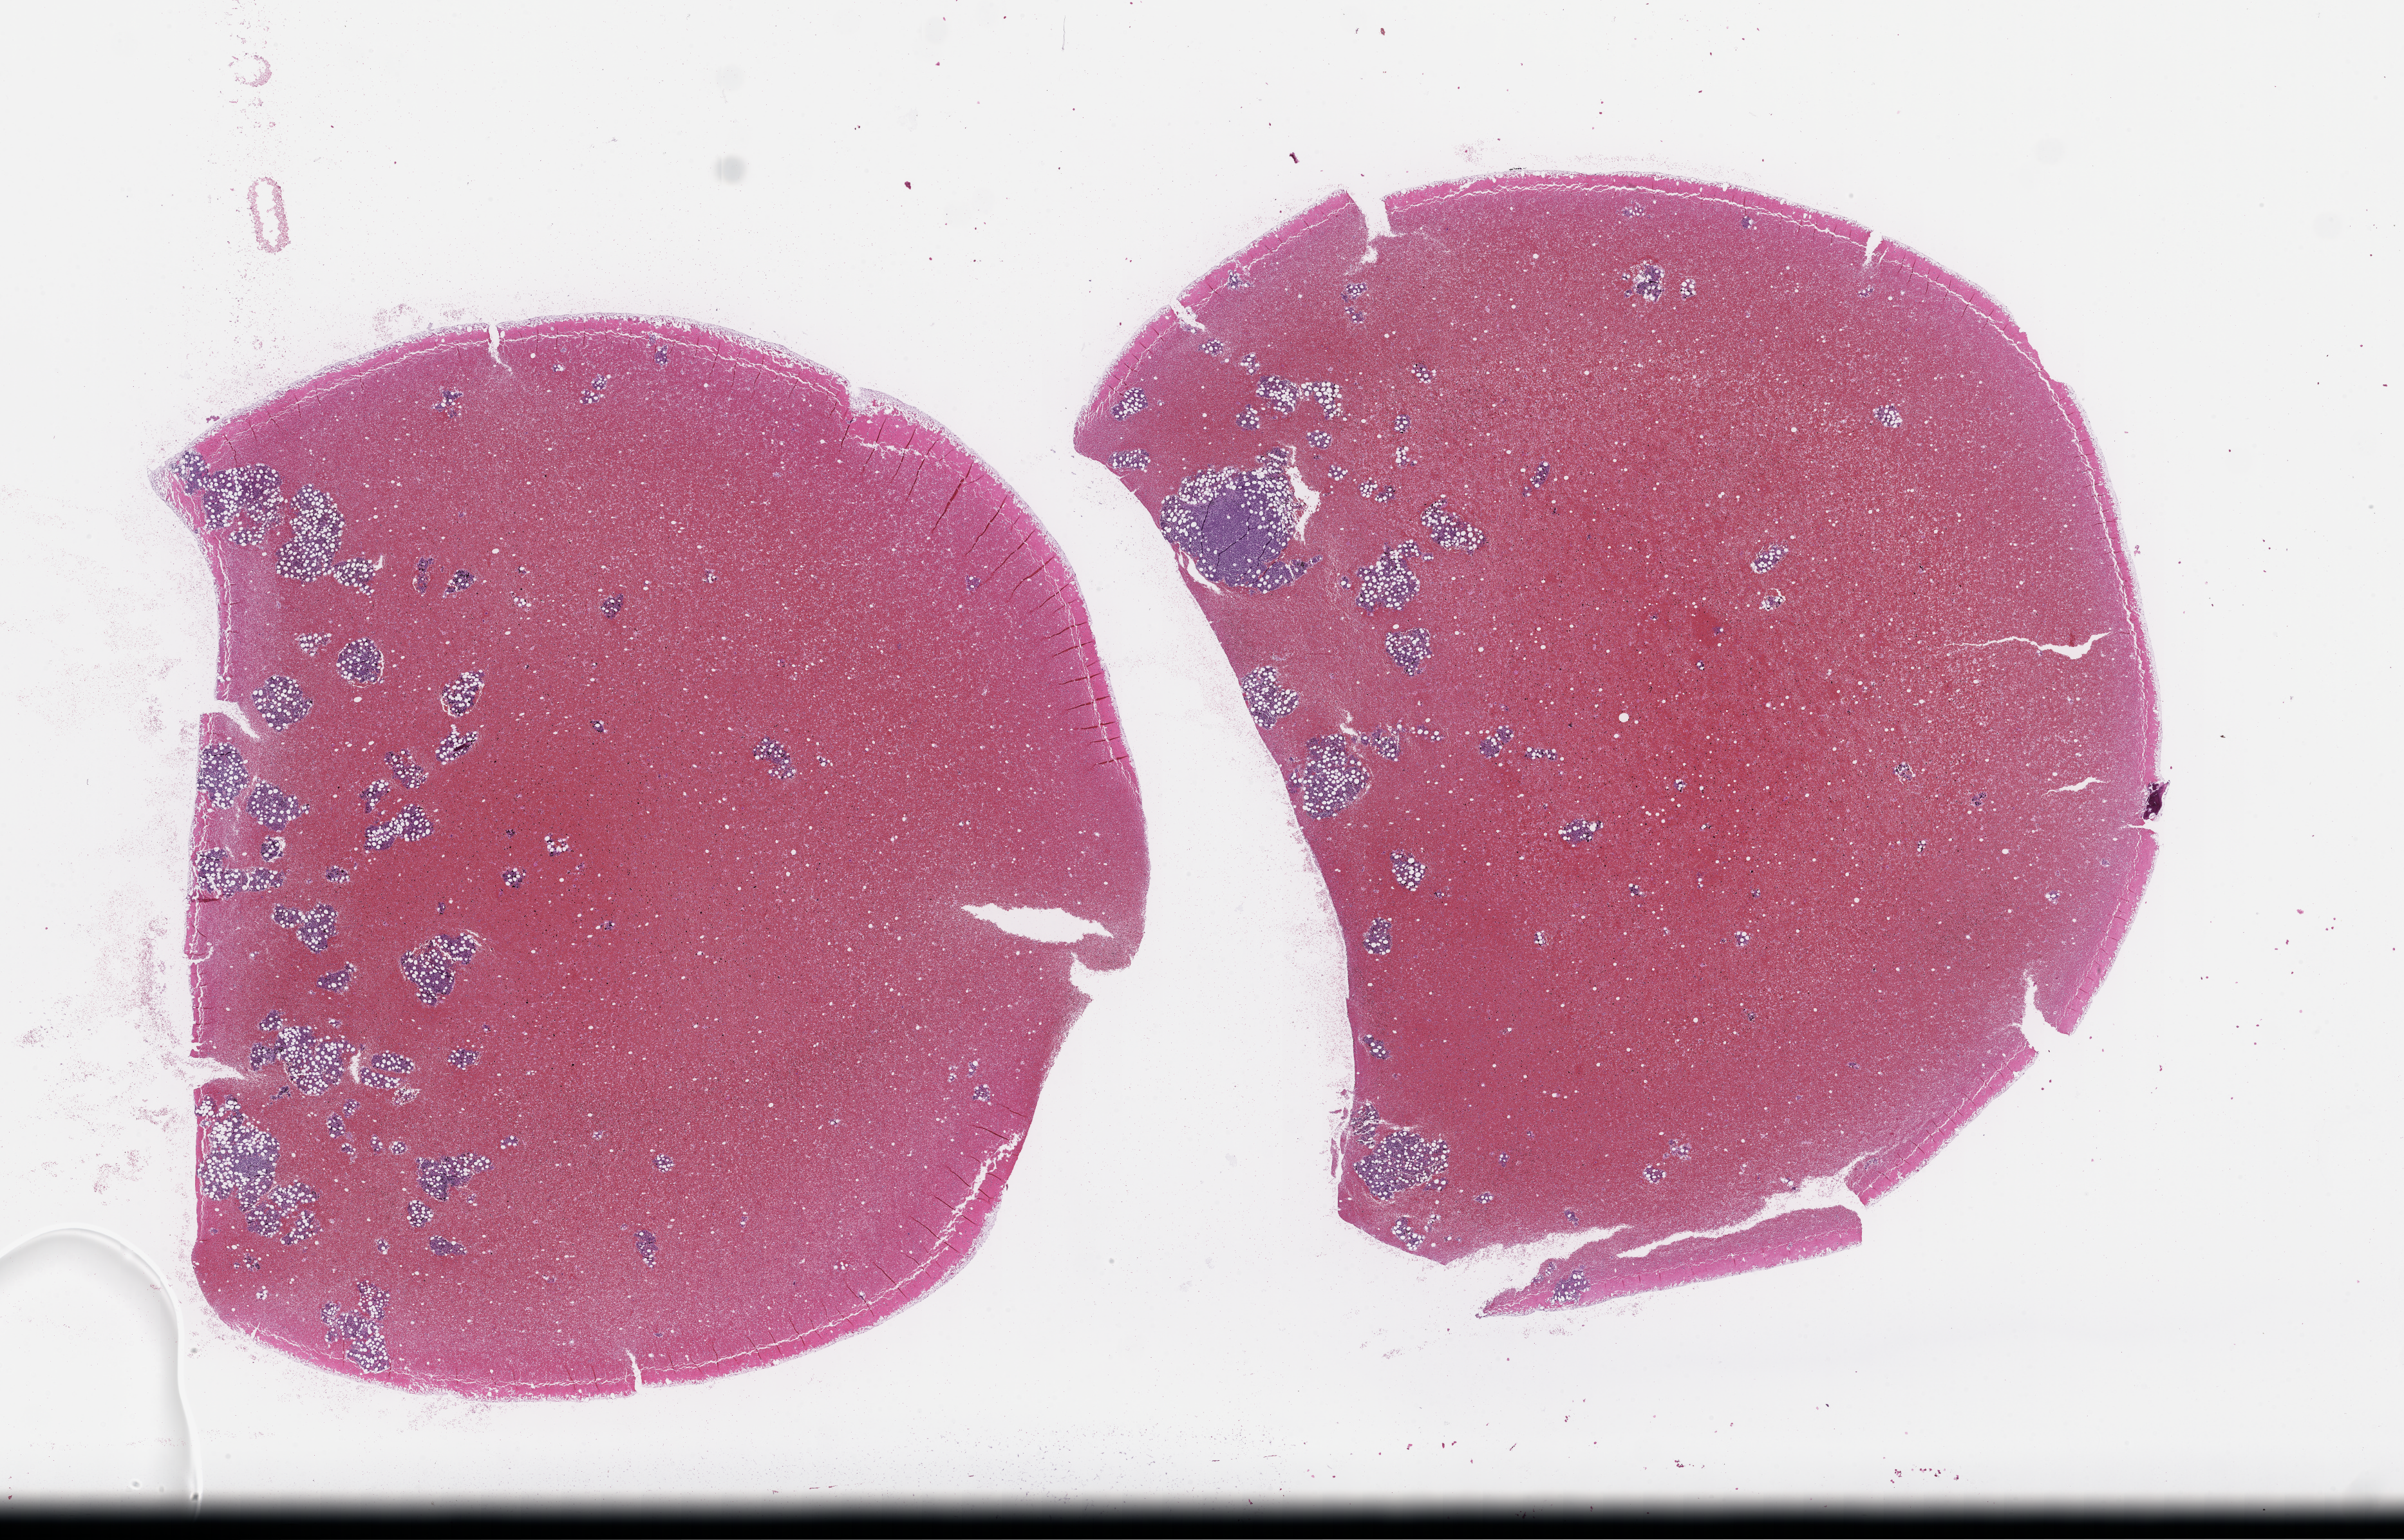
Whole-slide image, haematoxylin and eosin stain — low-resolution overview of the scanned area, about 30.2 x 19.3 mm, formalin-fixed, paraffin-embedded (FFPE) tissue, site: bone marrow, archival tissue. Male patient.
This section: primary tumor. Diagnosis: Plasma Cell Myeloma.